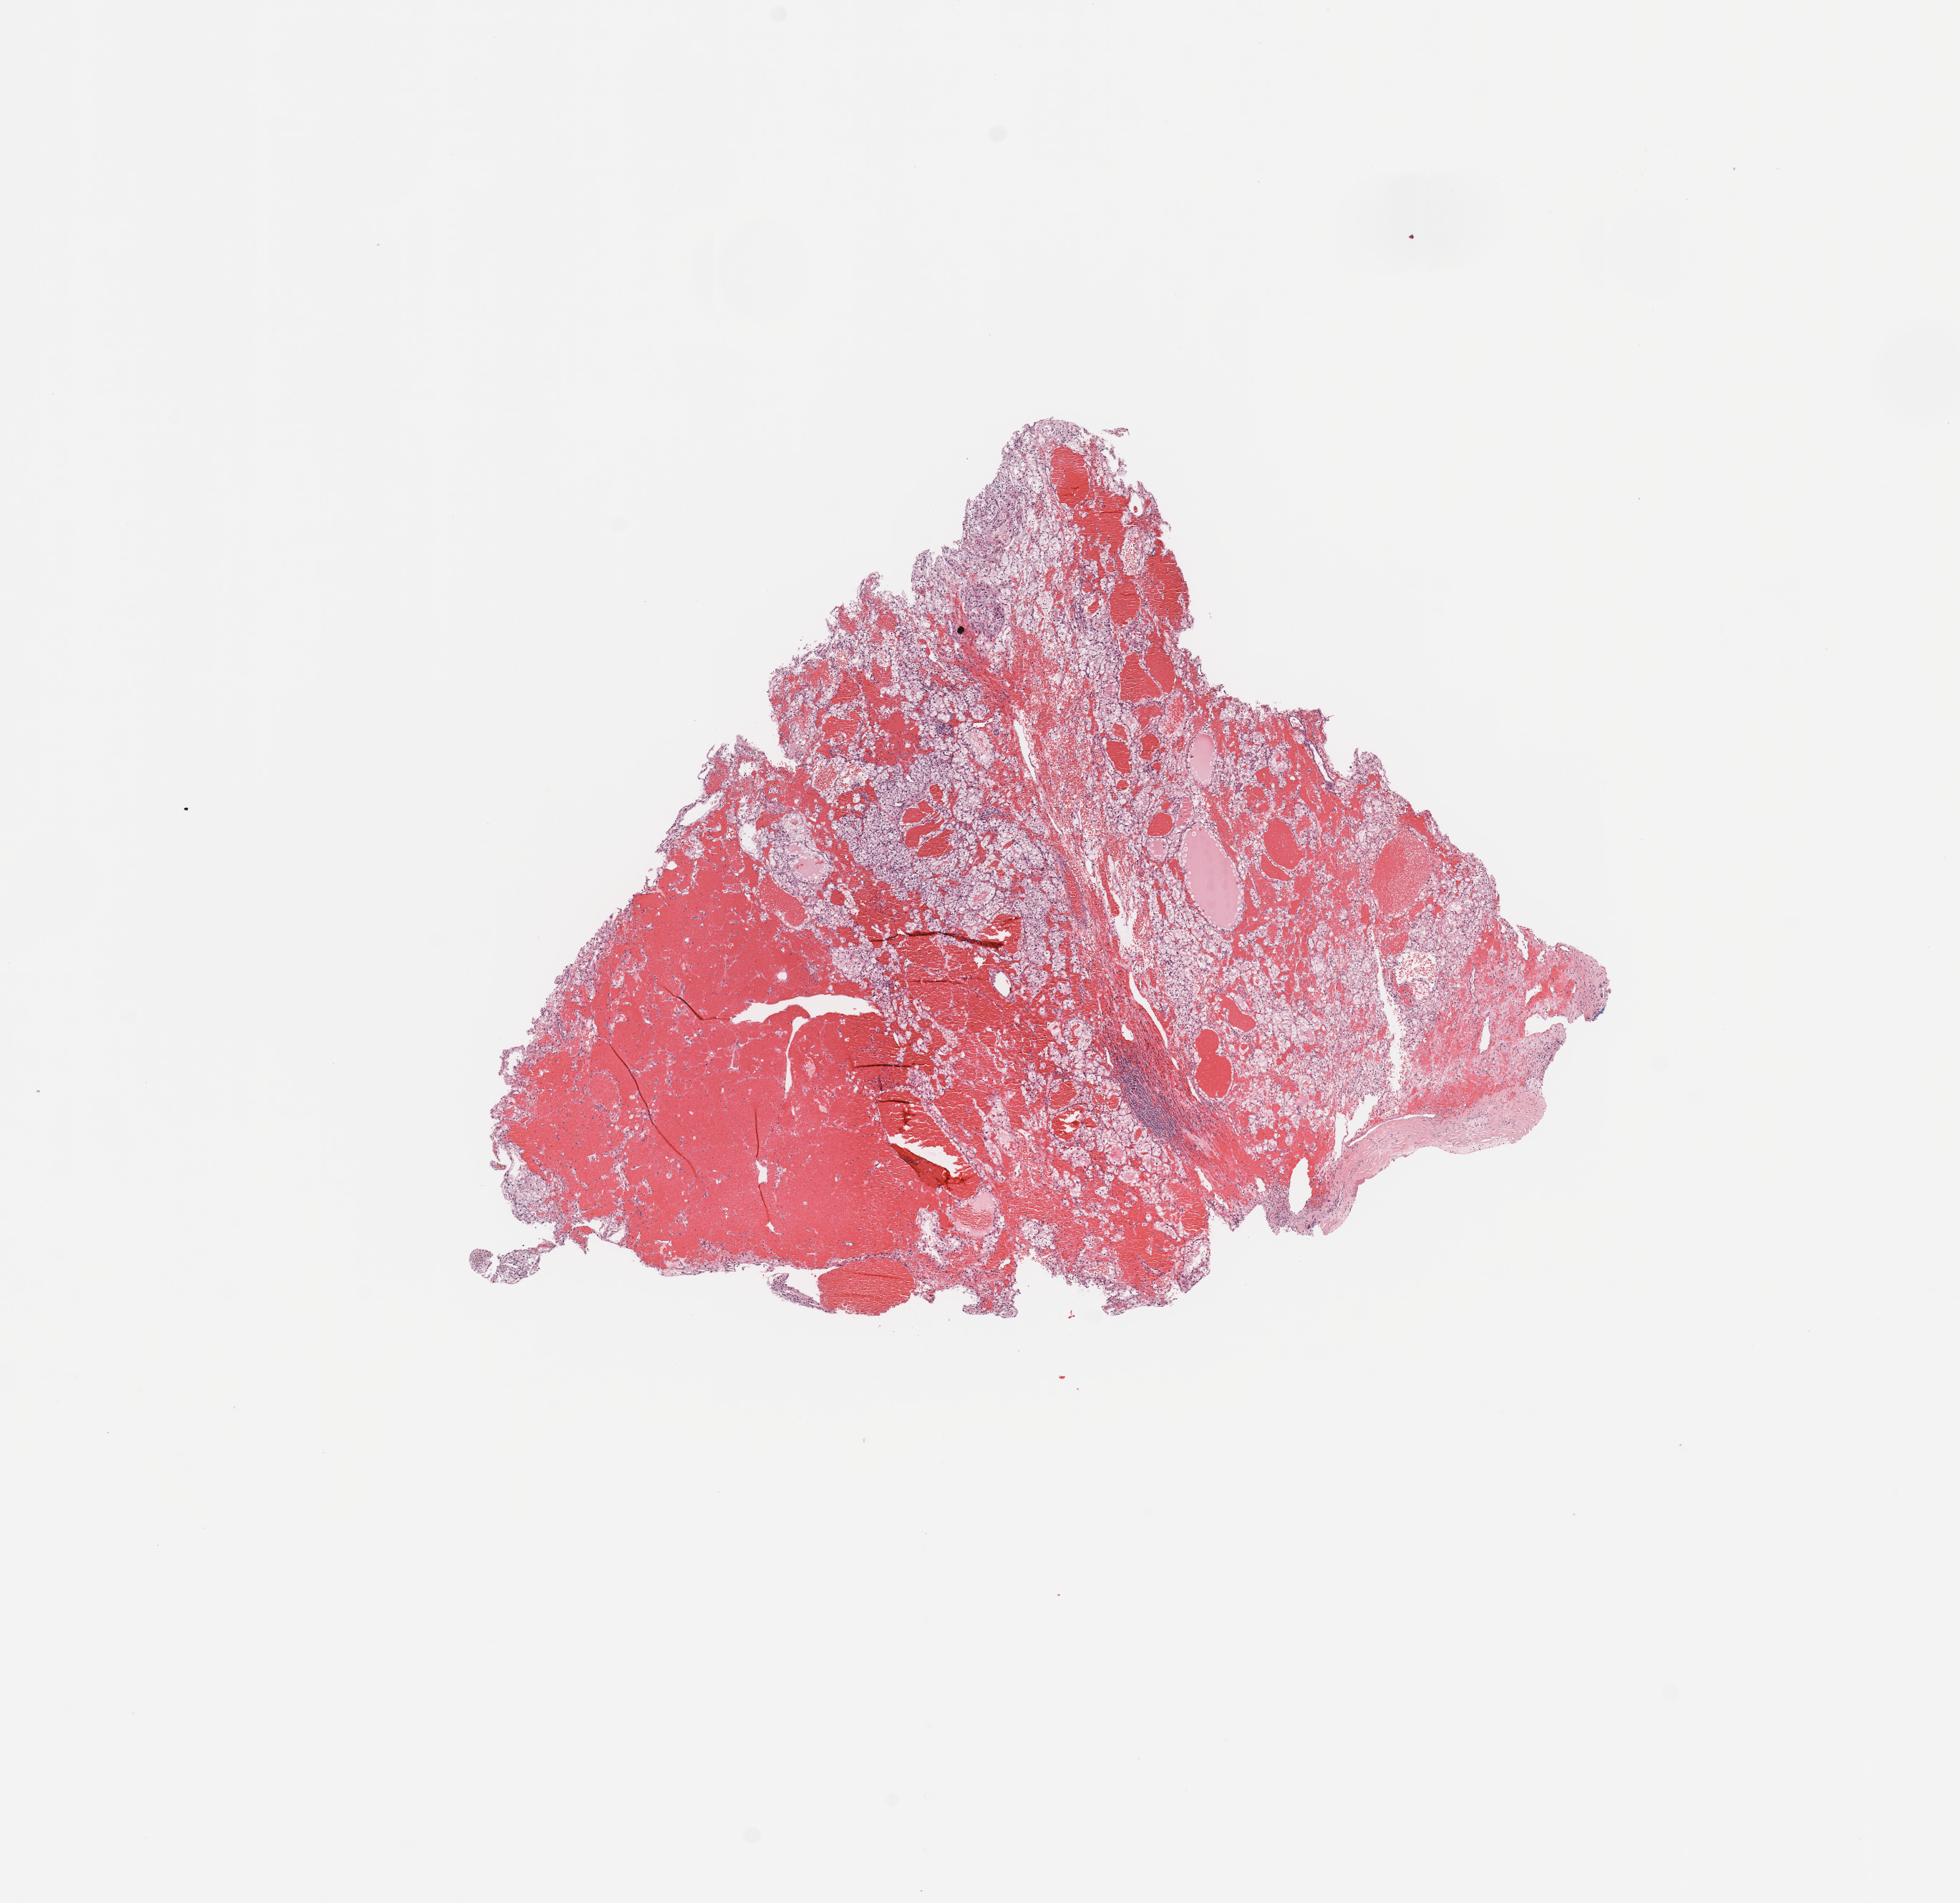
Whole-slide histology image, H&E-stained, shown as a low-resolution overview of the whole scanned area (about 10.8 x 10.5 mm). Tumour tissue sample, sampled site: kidney. Patient: female, age 68 years.
Diagnosis: Renal cell carcinoma, NOS.